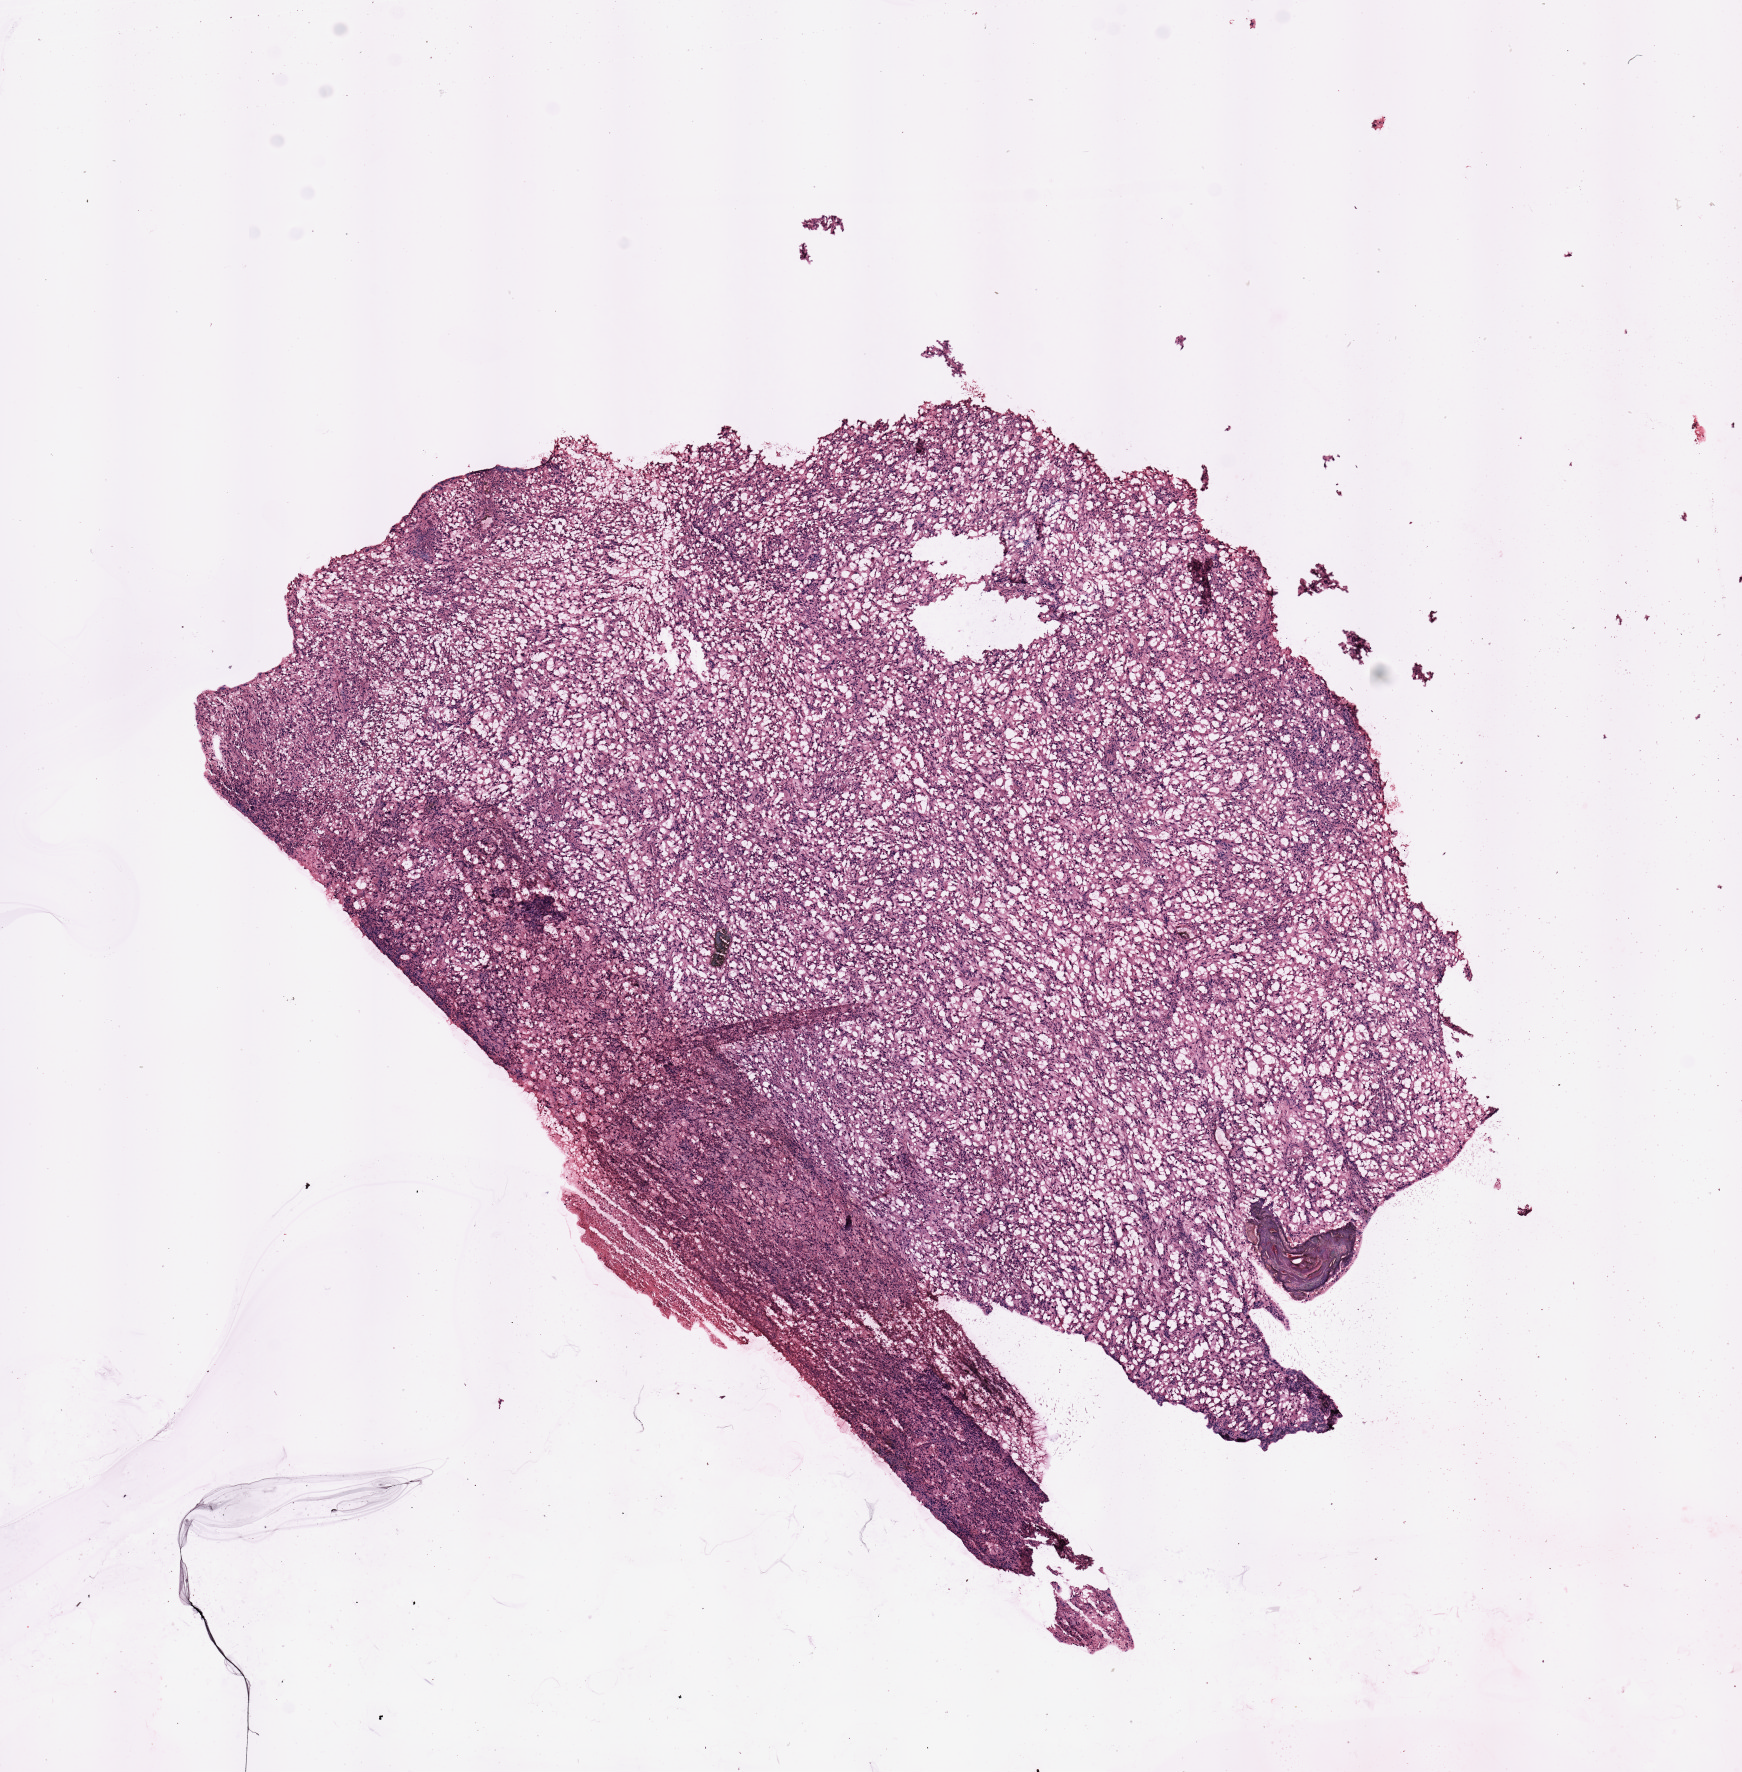
Whole-slide histology image, H&E — shown as a low-resolution overview of the whole scanned area (about 13.8 x 14.0 mm, acquisition: 20x scan), tumour tissue sample. Patient: male, age 74 years.
Patient diagnosis (cohort enrolment): sarcoma (site not recorded at cohort level).